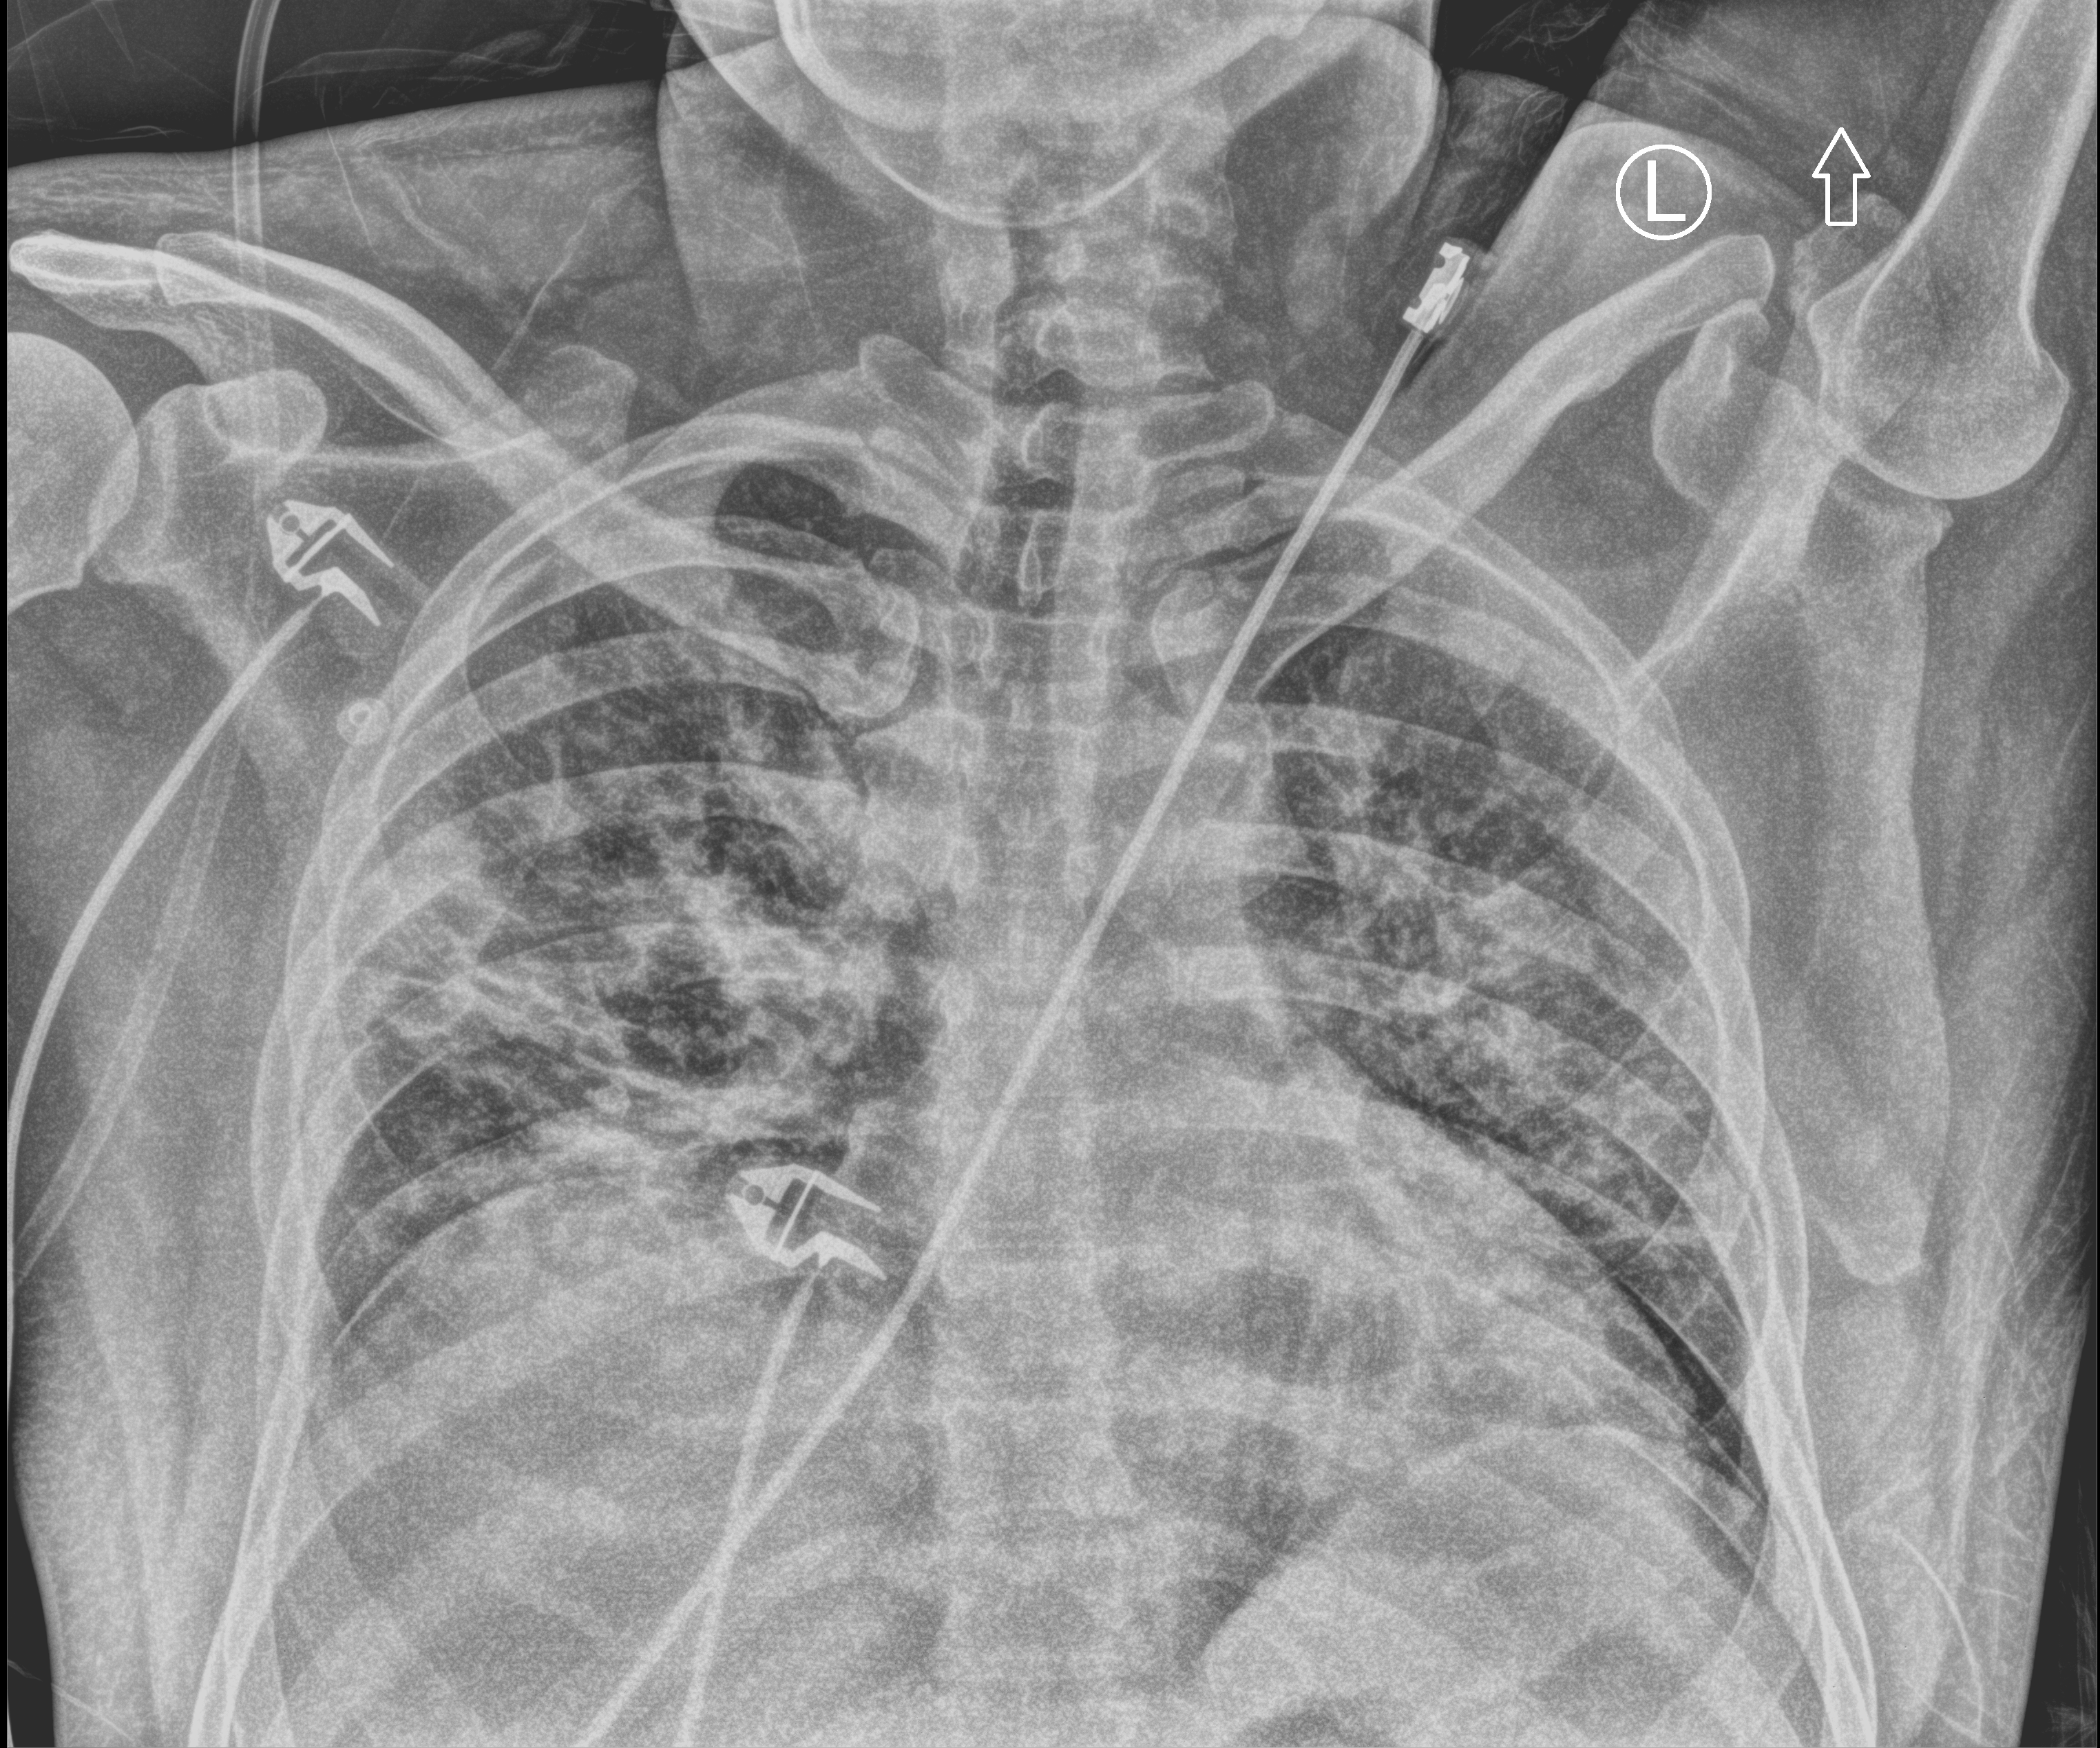
Chest X-ray (portable); anteroposterior (AP) projection. Male patient hospitalised with COVID-19, age 18–59 years.
Hospital-stay facts (about this admission, not read from this image; timing relative to this image not recorded): mechanically ventilated during this hospital stay: yes.